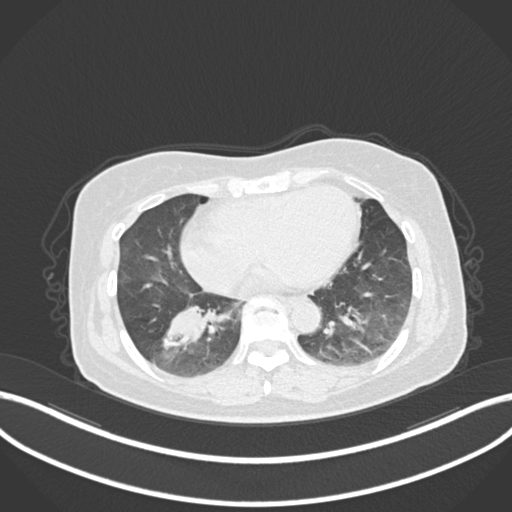
Chest CT, one axial slice. Position 48 of 222 along the scan axis. Reconstruction kernel B30f. 120 kVp. Lung window (W 1500 / L -600 HU). 1 mm slice thickness. 512 × 512 image matrix. Patient: female, 67 years. From the clinical record (not read from this slice): clinical TNM (as recorded): T1c N1 M0; histopathological grade: G2-3.
Outlined on this slice (bounding box drawn by a radiologist):
- lung tumour (recorded histology: adenocarcinoma): bounding box [x1, y1, x2, y2] px = [152, 296, 221, 357]